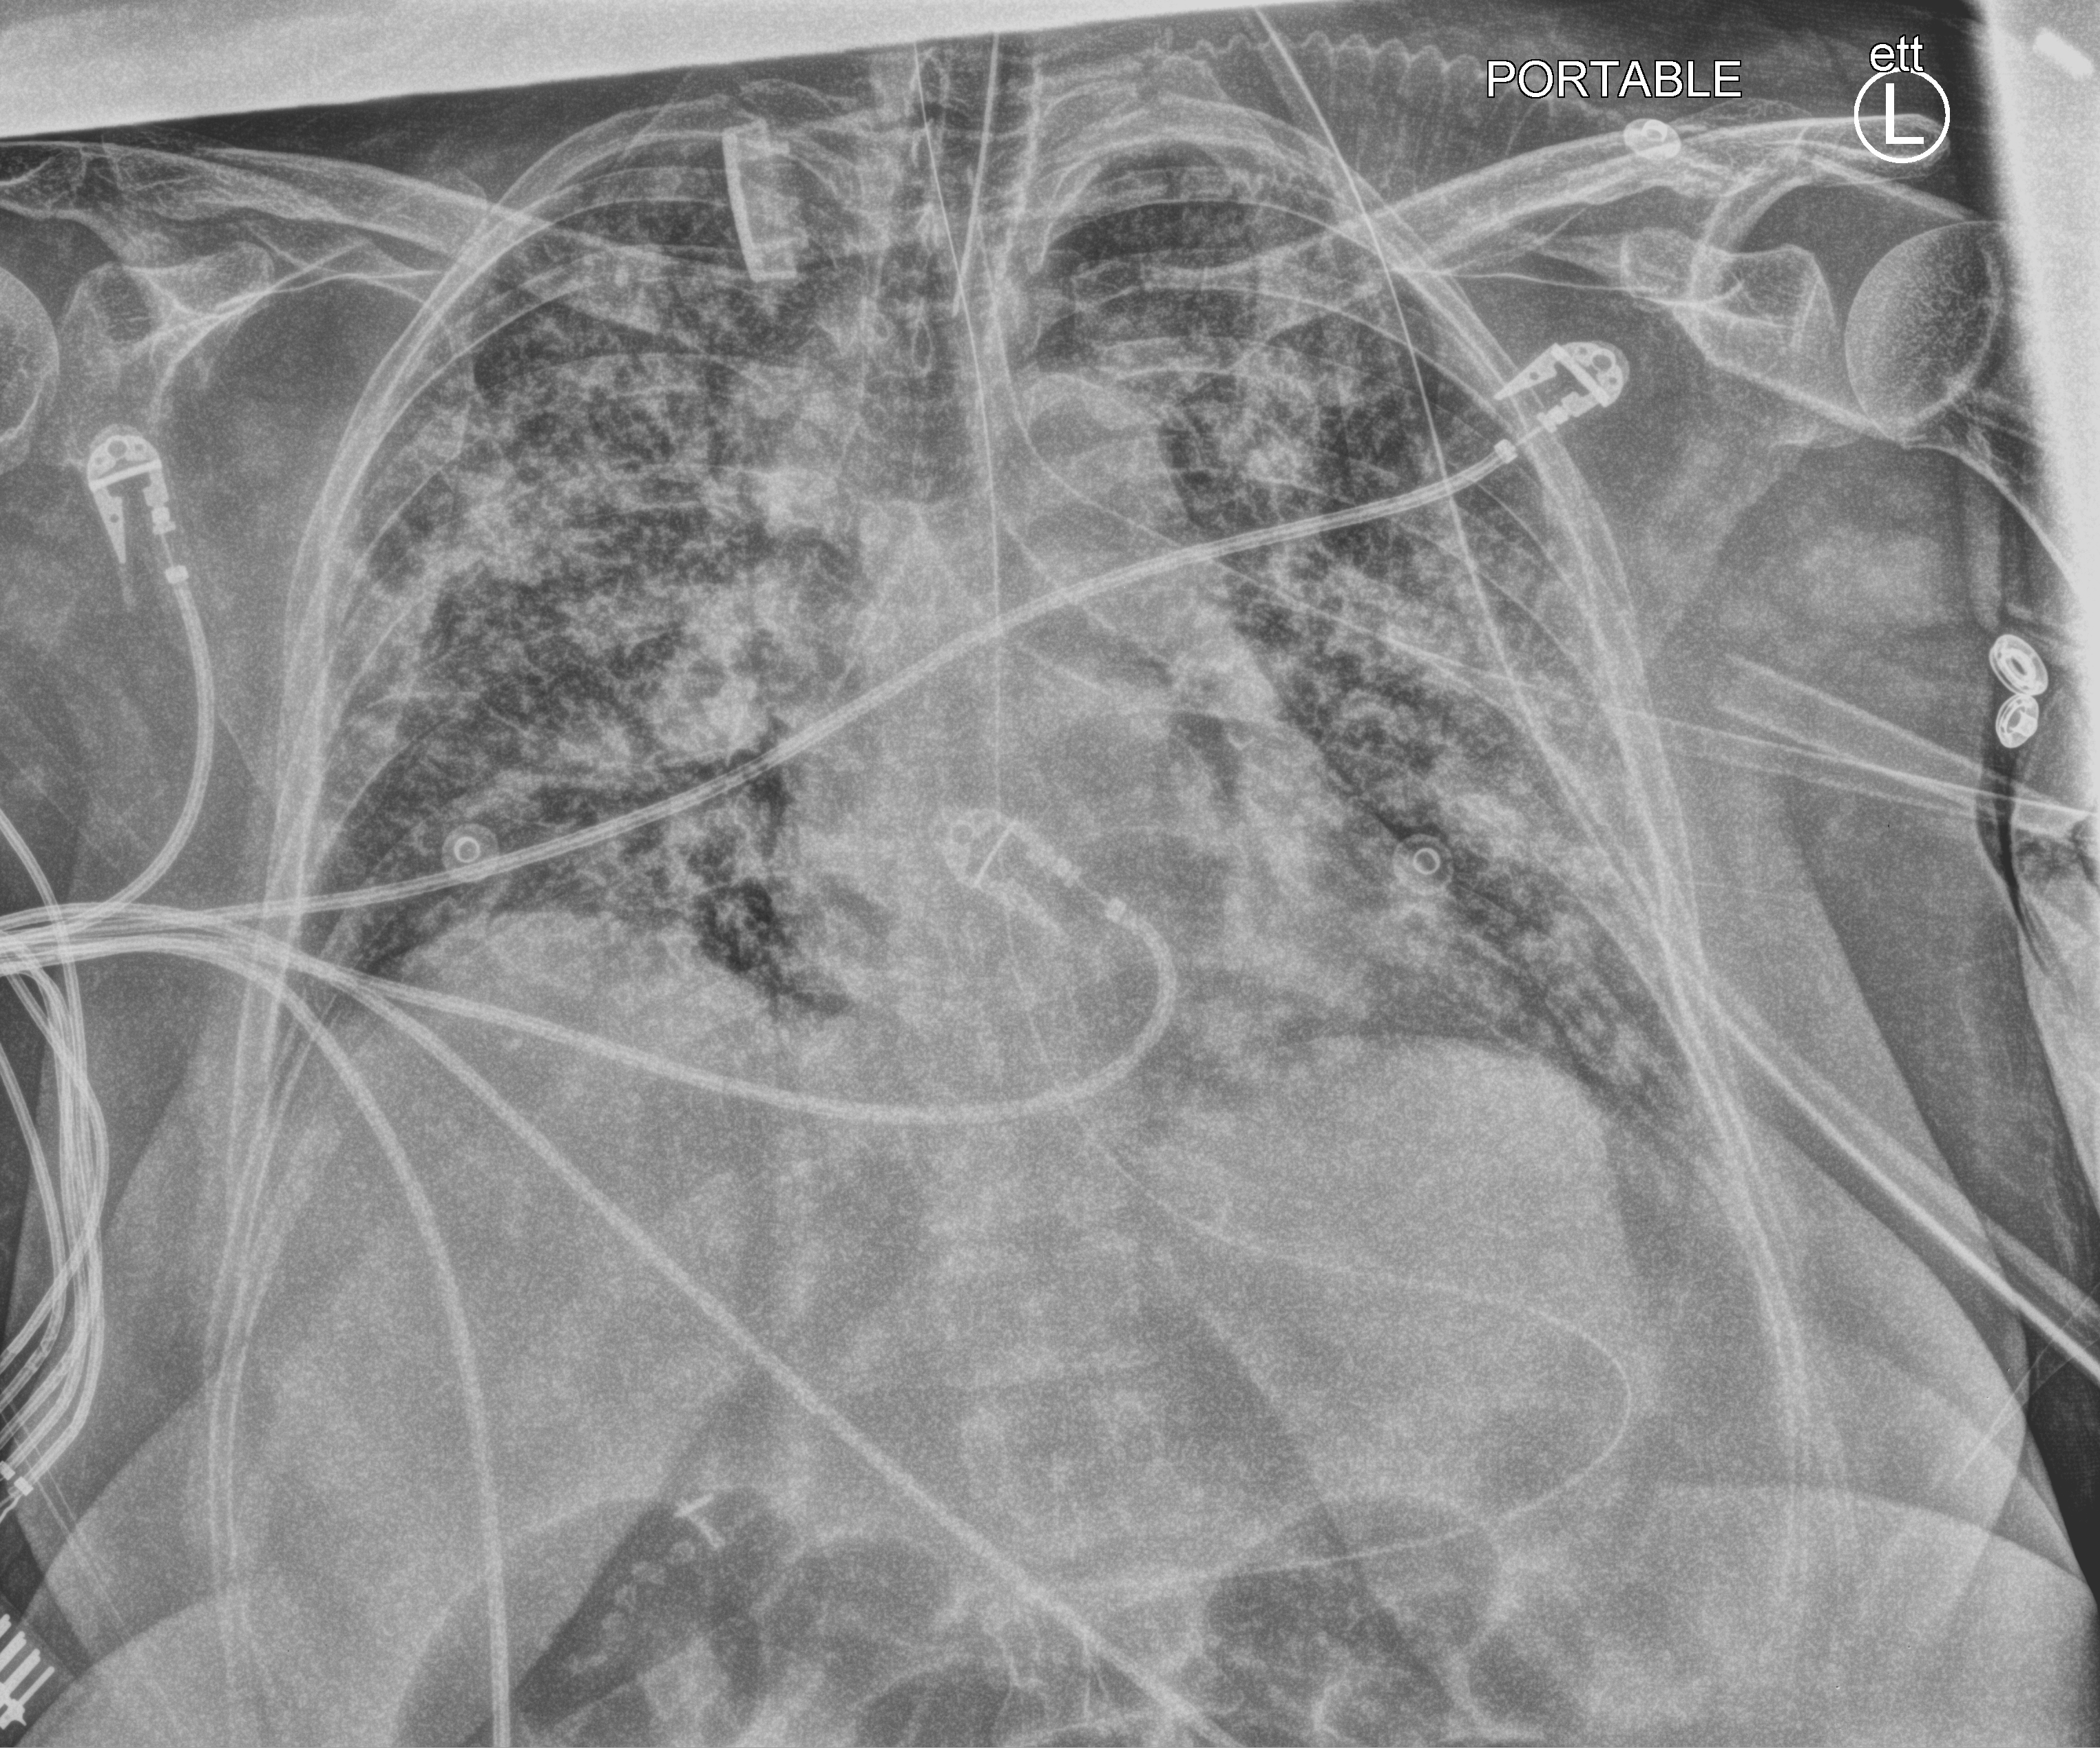
Chest X-ray (portable); anteroposterior (AP) projection. Female patient hospitalised with COVID-19, age 18–59 years.
Hospital-stay facts (about this admission, not read from this image; timing relative to this image not recorded): length of hospital stay: 22 days; hypertension (admission record): no.